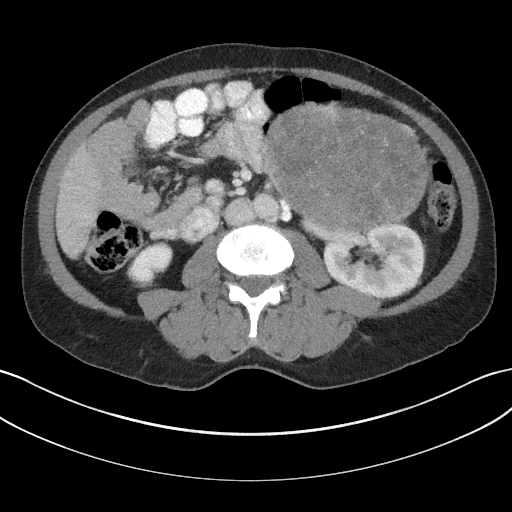
Contrast-enhanced abdominal CT, one axial slice. Position 81 of 147 along the scan axis. Reconstruction kernel I31f/3. Soft-tissue window (W 400 / L 40 HU). 3 mm slice thickness. 512 × 512 image matrix. Male patient, age 58 years. From the clinical record (not read from this slice): diagnosis: adrenocortical carcinoma; tumour side: left adrenal; tumour size at pathology: 22 cm.
Outlined on this slice (semi-automatic segmentation, software-assisted and operator-edited):
- mass: bounding box <266,106,427,228> (left, top, right, bottom; pixels)